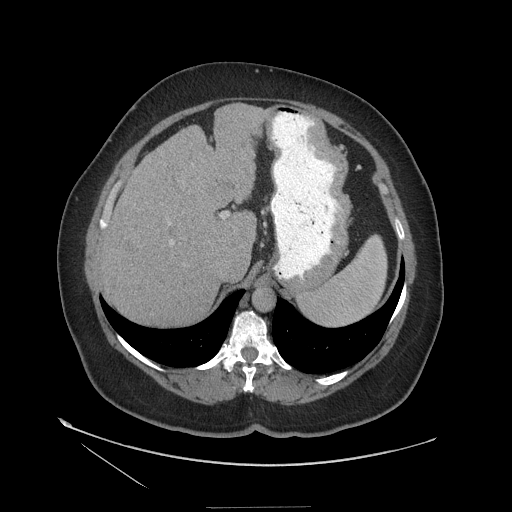
Contrast-enhanced abdominal CT (liver protocol), one axial slice. Position 85 of 127 along the scan axis. Reconstruction kernel STANDARD. Soft-tissue window (W 400 / L 40 HU). 2.5 mm slice thickness. 512 × 512 image matrix. From the clinical record (not read from this slice): diagnosis: hepatocellular carcinoma (patient treated with transarterial chemoembolisation; whether this scan precedes or follows treatment is not stated here); TNM stage (as recorded): Stage-II; Child-Pugh class: A; tumour differentiation: well differentiated; tumour nodularity: multinodular.
Annotated regions visible in this slice (semi-automatically segmented with operator editing):
- liver parenchyma outside the tumour (the mass and vessels are separate outlines, so this box may not span the whole liver): bounding box (x1, y1, x2, y2) in pixels: (98, 104, 270, 325)
- mass: (121, 234, 142, 256)
- liver vessels: (171, 212, 228, 244)